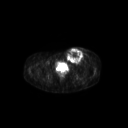
FDG PET of an extremity soft-tissue mass (from a PET/CT study), one axial slice; 3.27 mm slice thickness; 128 × 128 image matrix. Patient: female, 24 years. From the clinical record (not read from this slice): histological type: leiomyosarcoma; grade: high; site of the primary tumour: groin.
Annotated regions visible in this slice (expert contour drawn on MRI and transferred to this co-registered scan by the dataset authors):
- gross tumour volume including surrounding oedema: bounding box <65,47,91,64> (left, top, right, bottom; pixels)
- gross tumour volume (mass): <65,48,84,64>